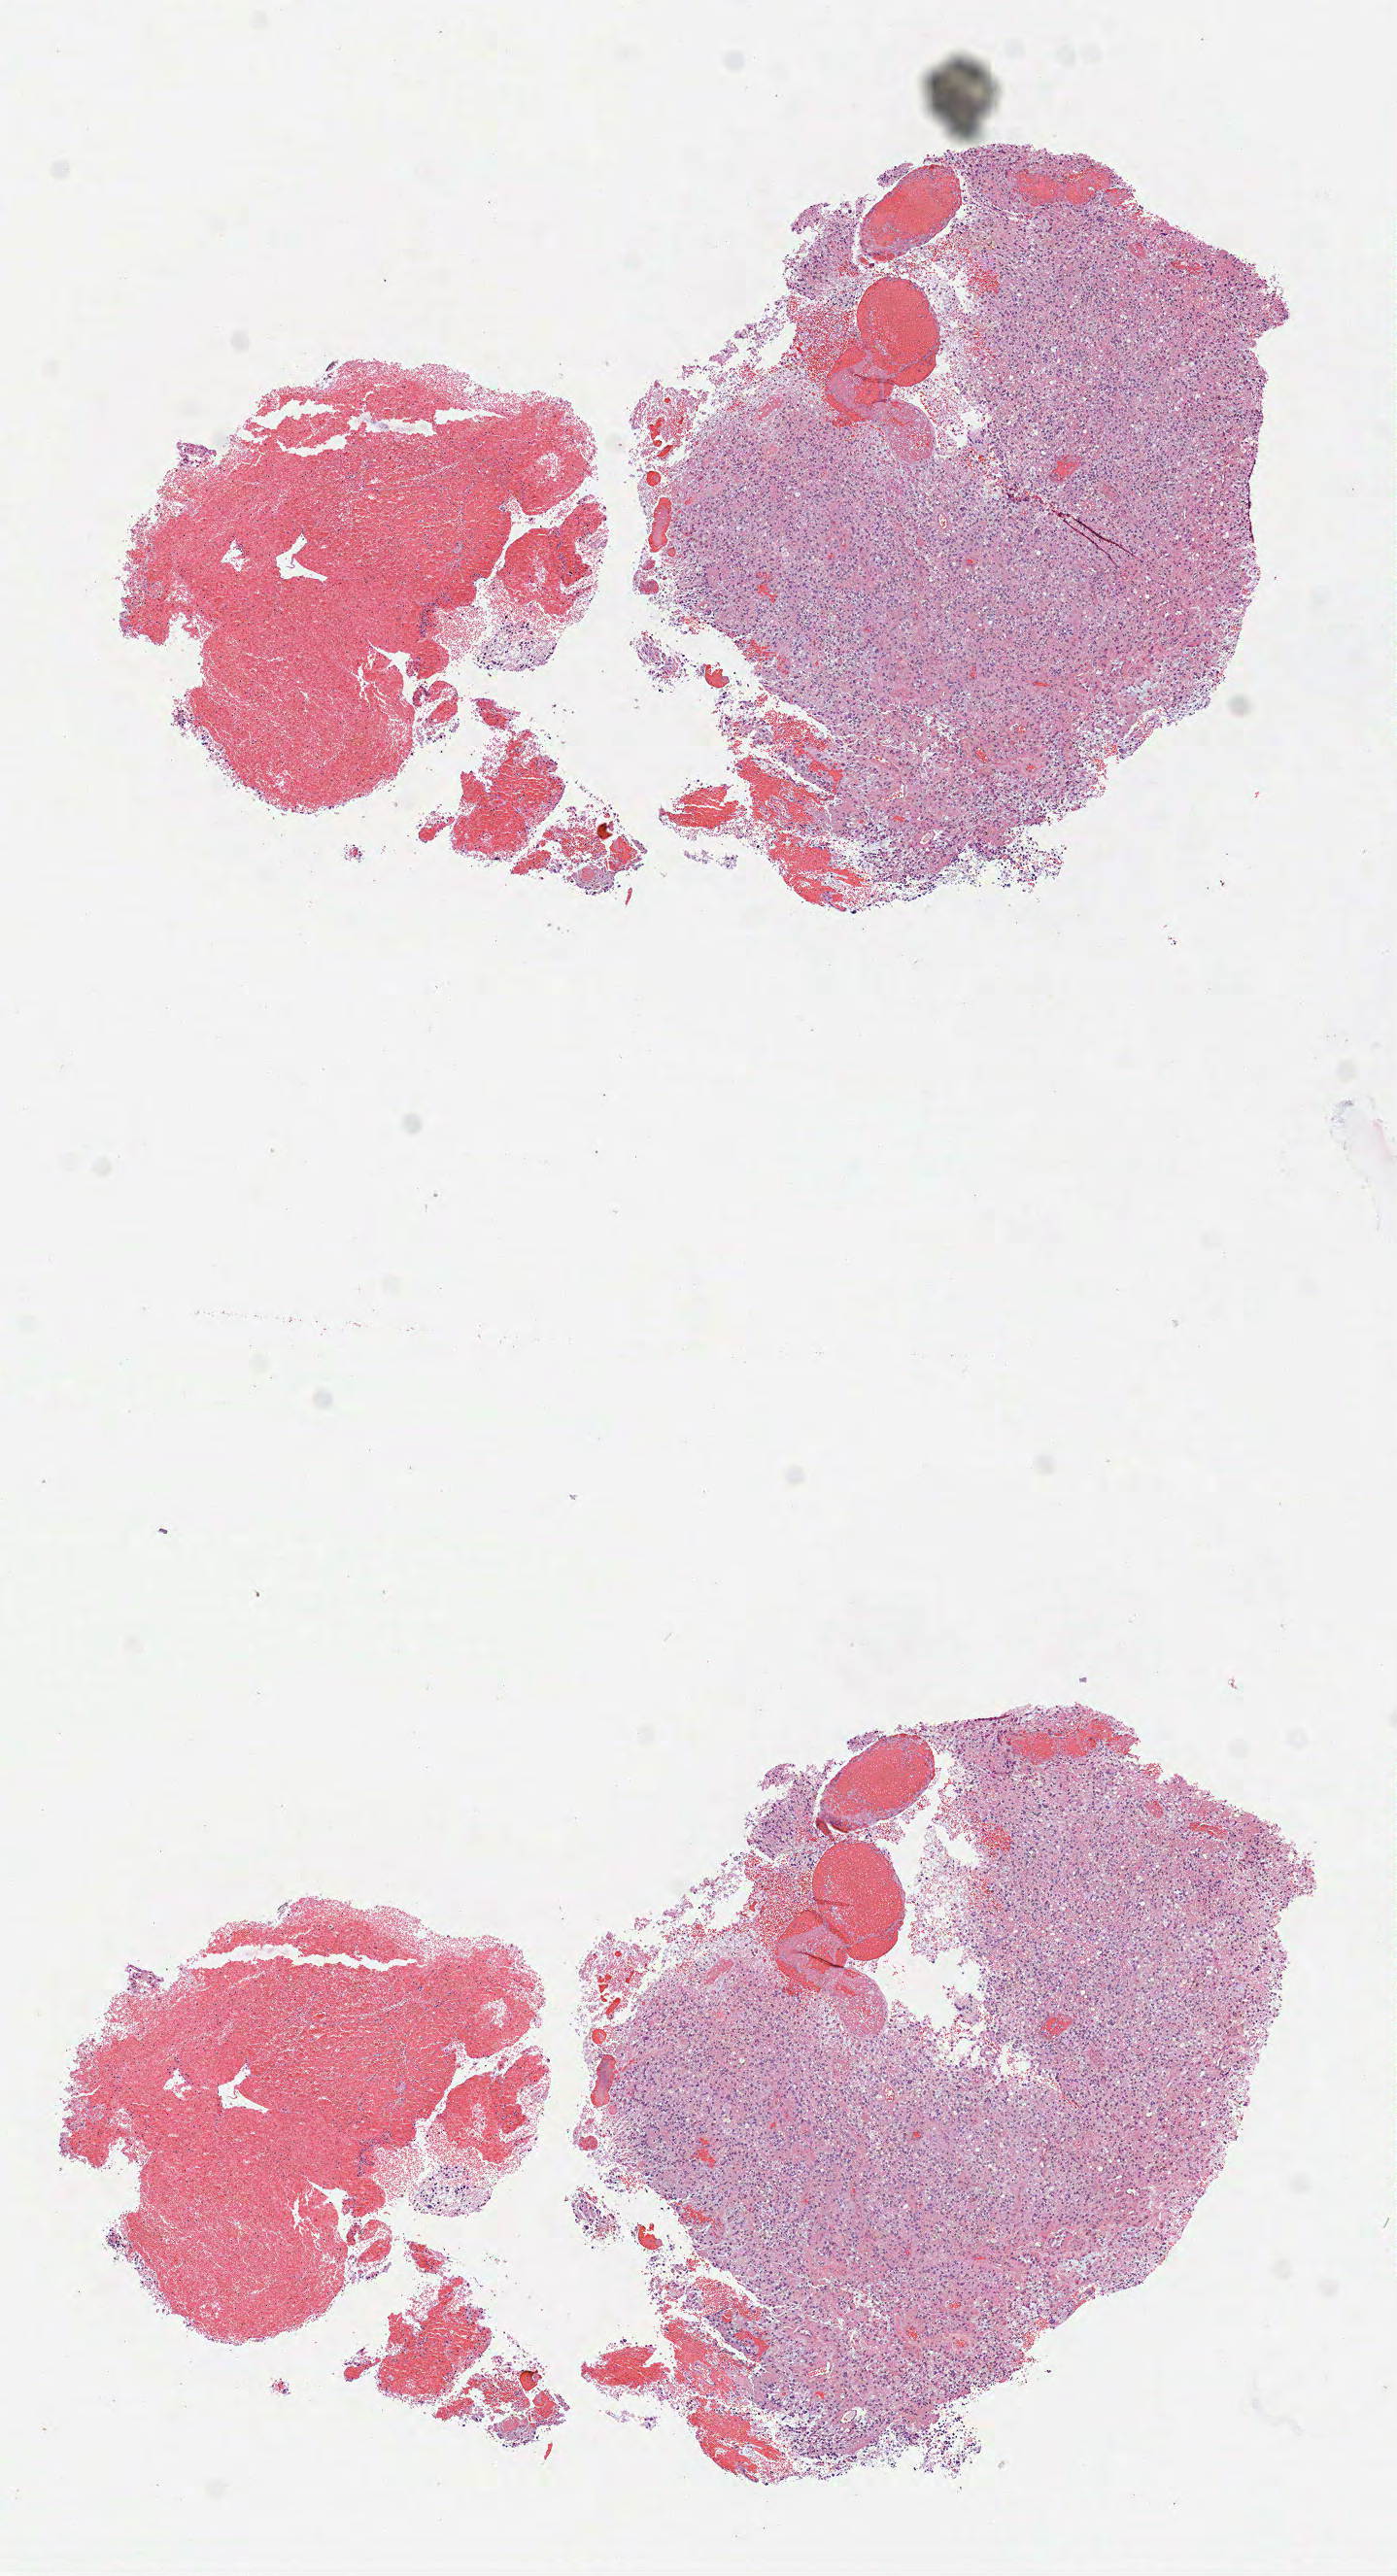
Whole-slide histology image, H&E, whole scanned area (about 5.8 x 10.7 mm, slide scanned at 40x) shown as a low-resolution overview. Formalin-fixed paraffin-embedded (FFPE) diagnostic section. Primary tumour sample from the brain. Male patient; age at initial diagnosis 58 years.
Histologic diagnosis: Glioblastoma.